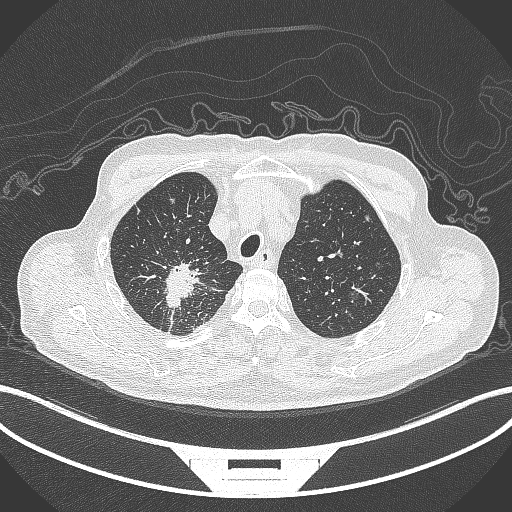
Chest CT, one axial slice. Reconstruction kernel B70f. 120 kVp. Lung window (W 1500 / L -600 HU). 1 mm slice thickness. 512 × 512 image matrix. Male patient, age 69 years. Case-level facts recorded for this patient, not image findings: clinical TNM (as recorded): T1c N1 M1.
Structures marked on this image (rectangle marked by the reading radiologist):
- lung tumour (recorded histology: adenocarcinoma): box from (x=156, y=260) to (x=209, y=318) px